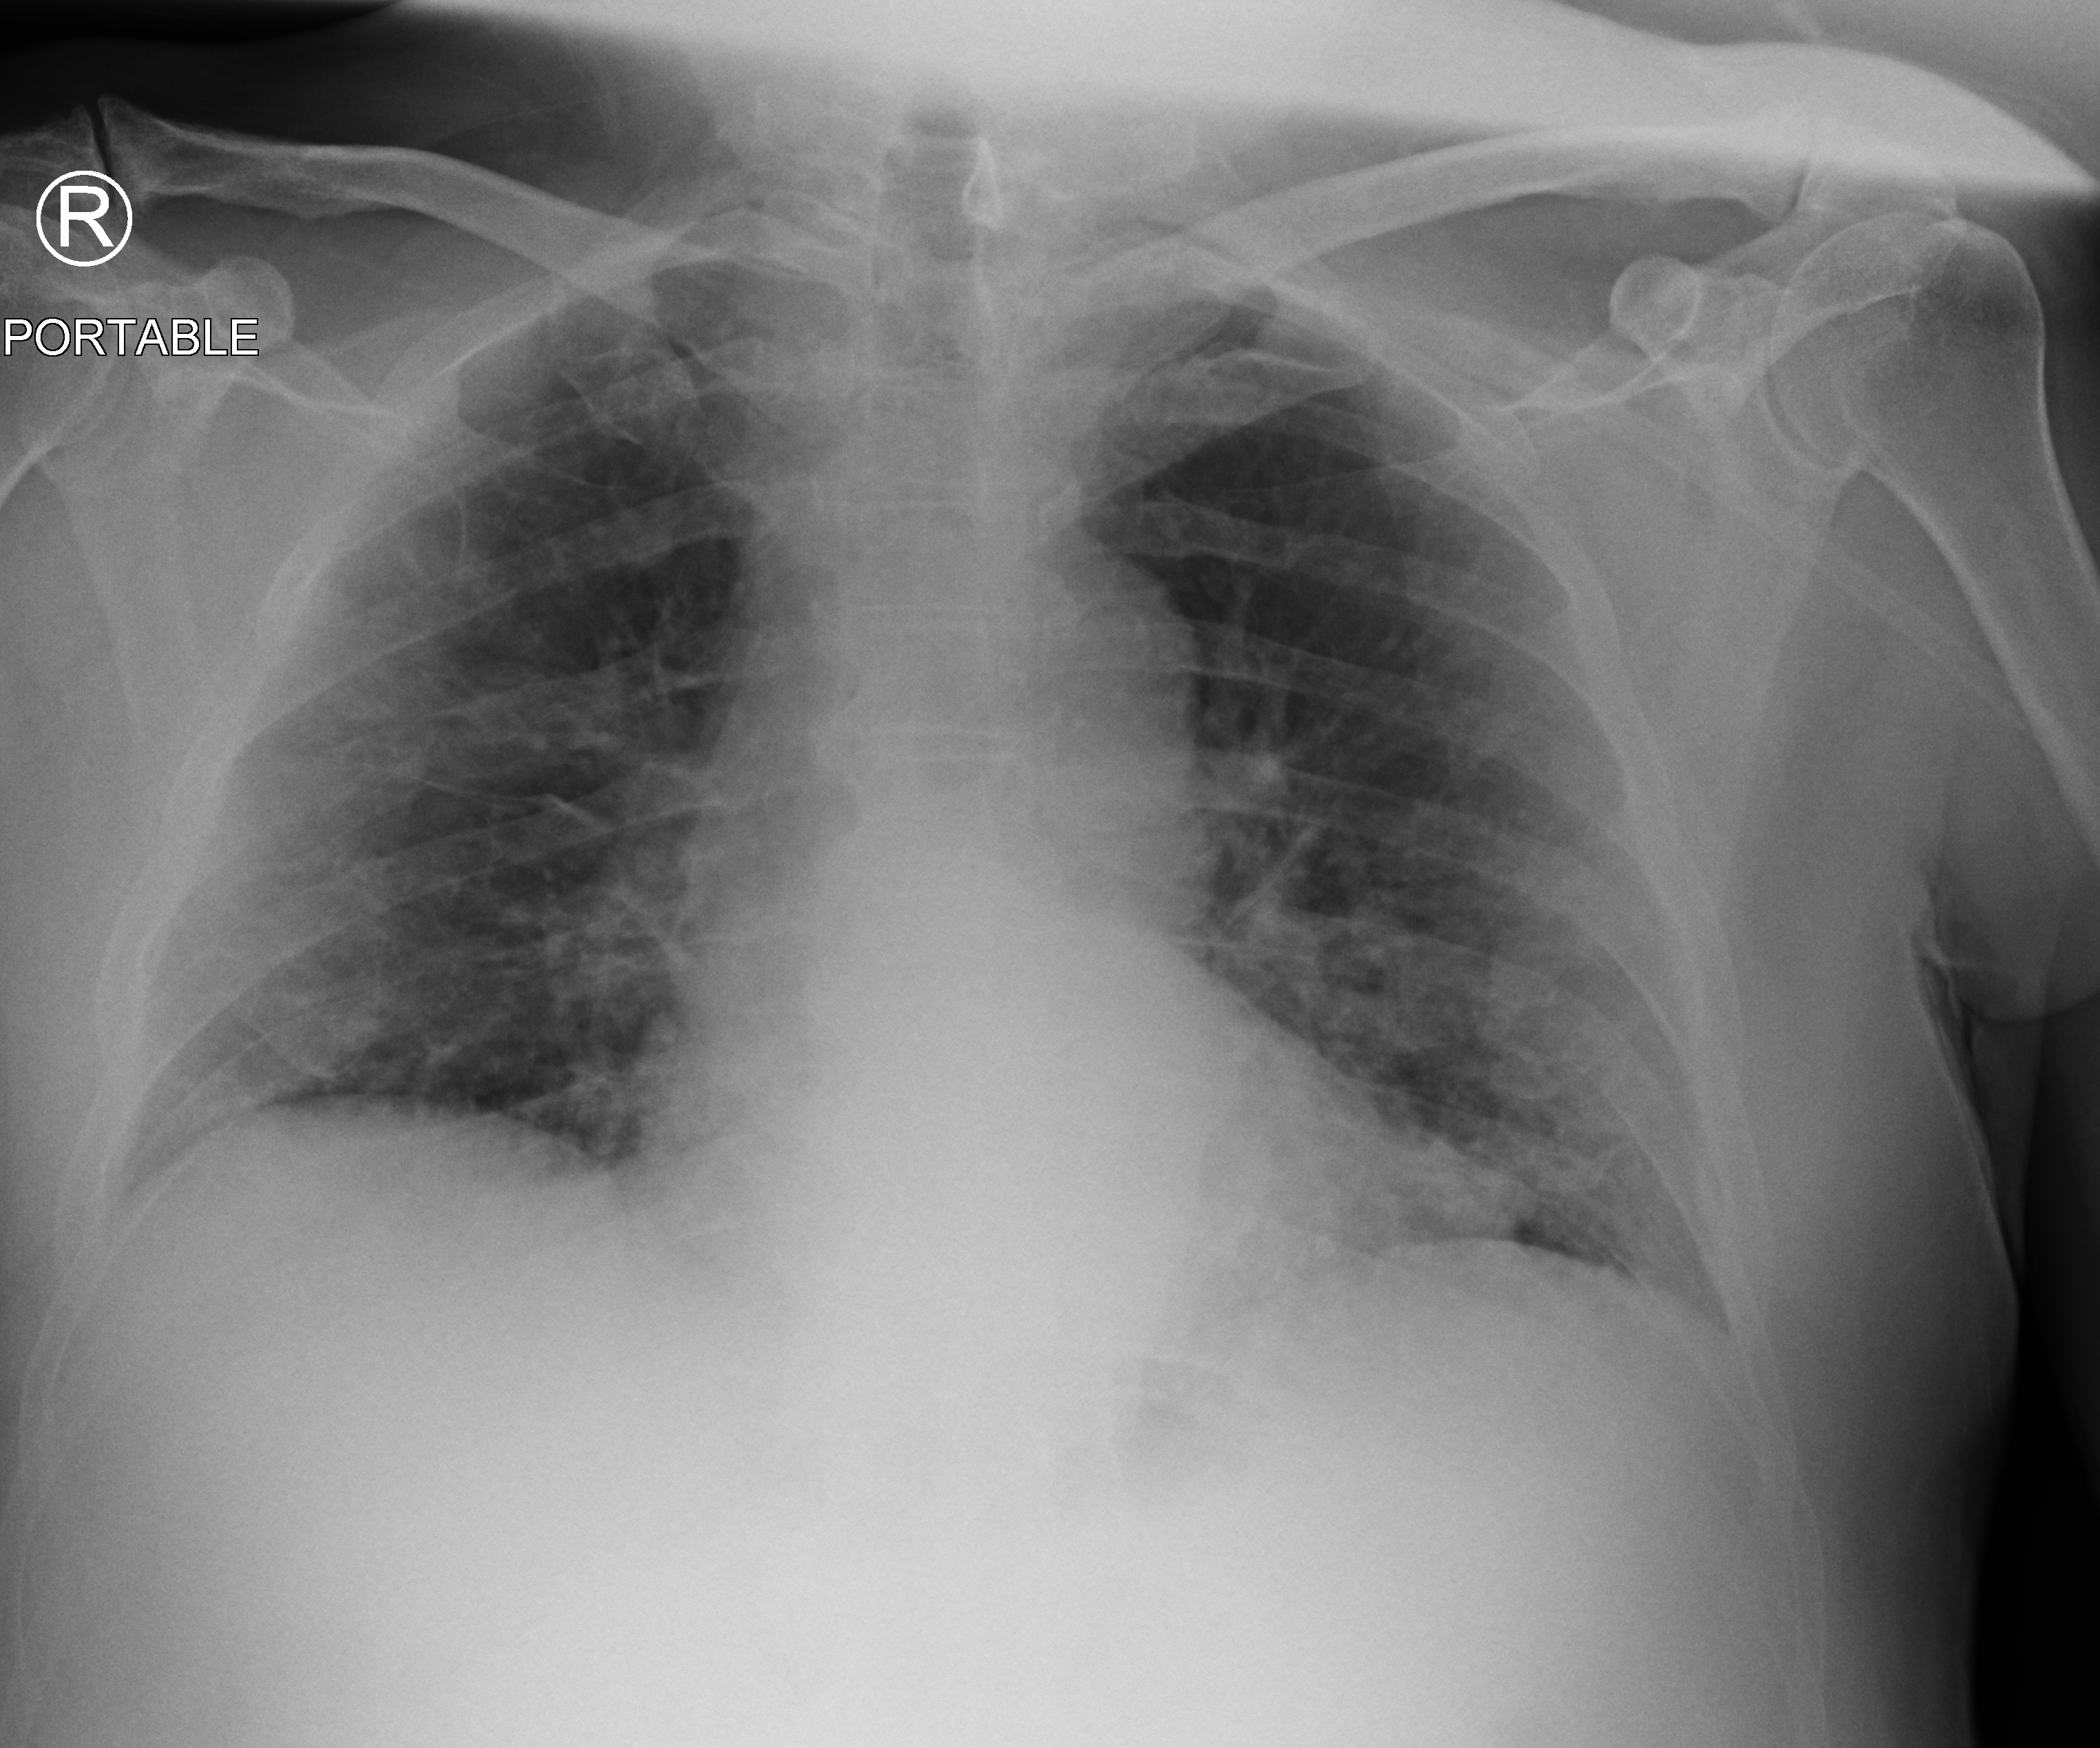
Chest X-ray (portable), anteroposterior (AP) projection. Male patient hospitalised with COVID-19, age 60–74 years.
Admission-level facts for this patient (not findings on this image; timing relative to this image not recorded): other chronic lung disease (admission record): no; mechanically ventilated during this hospital stay: no.